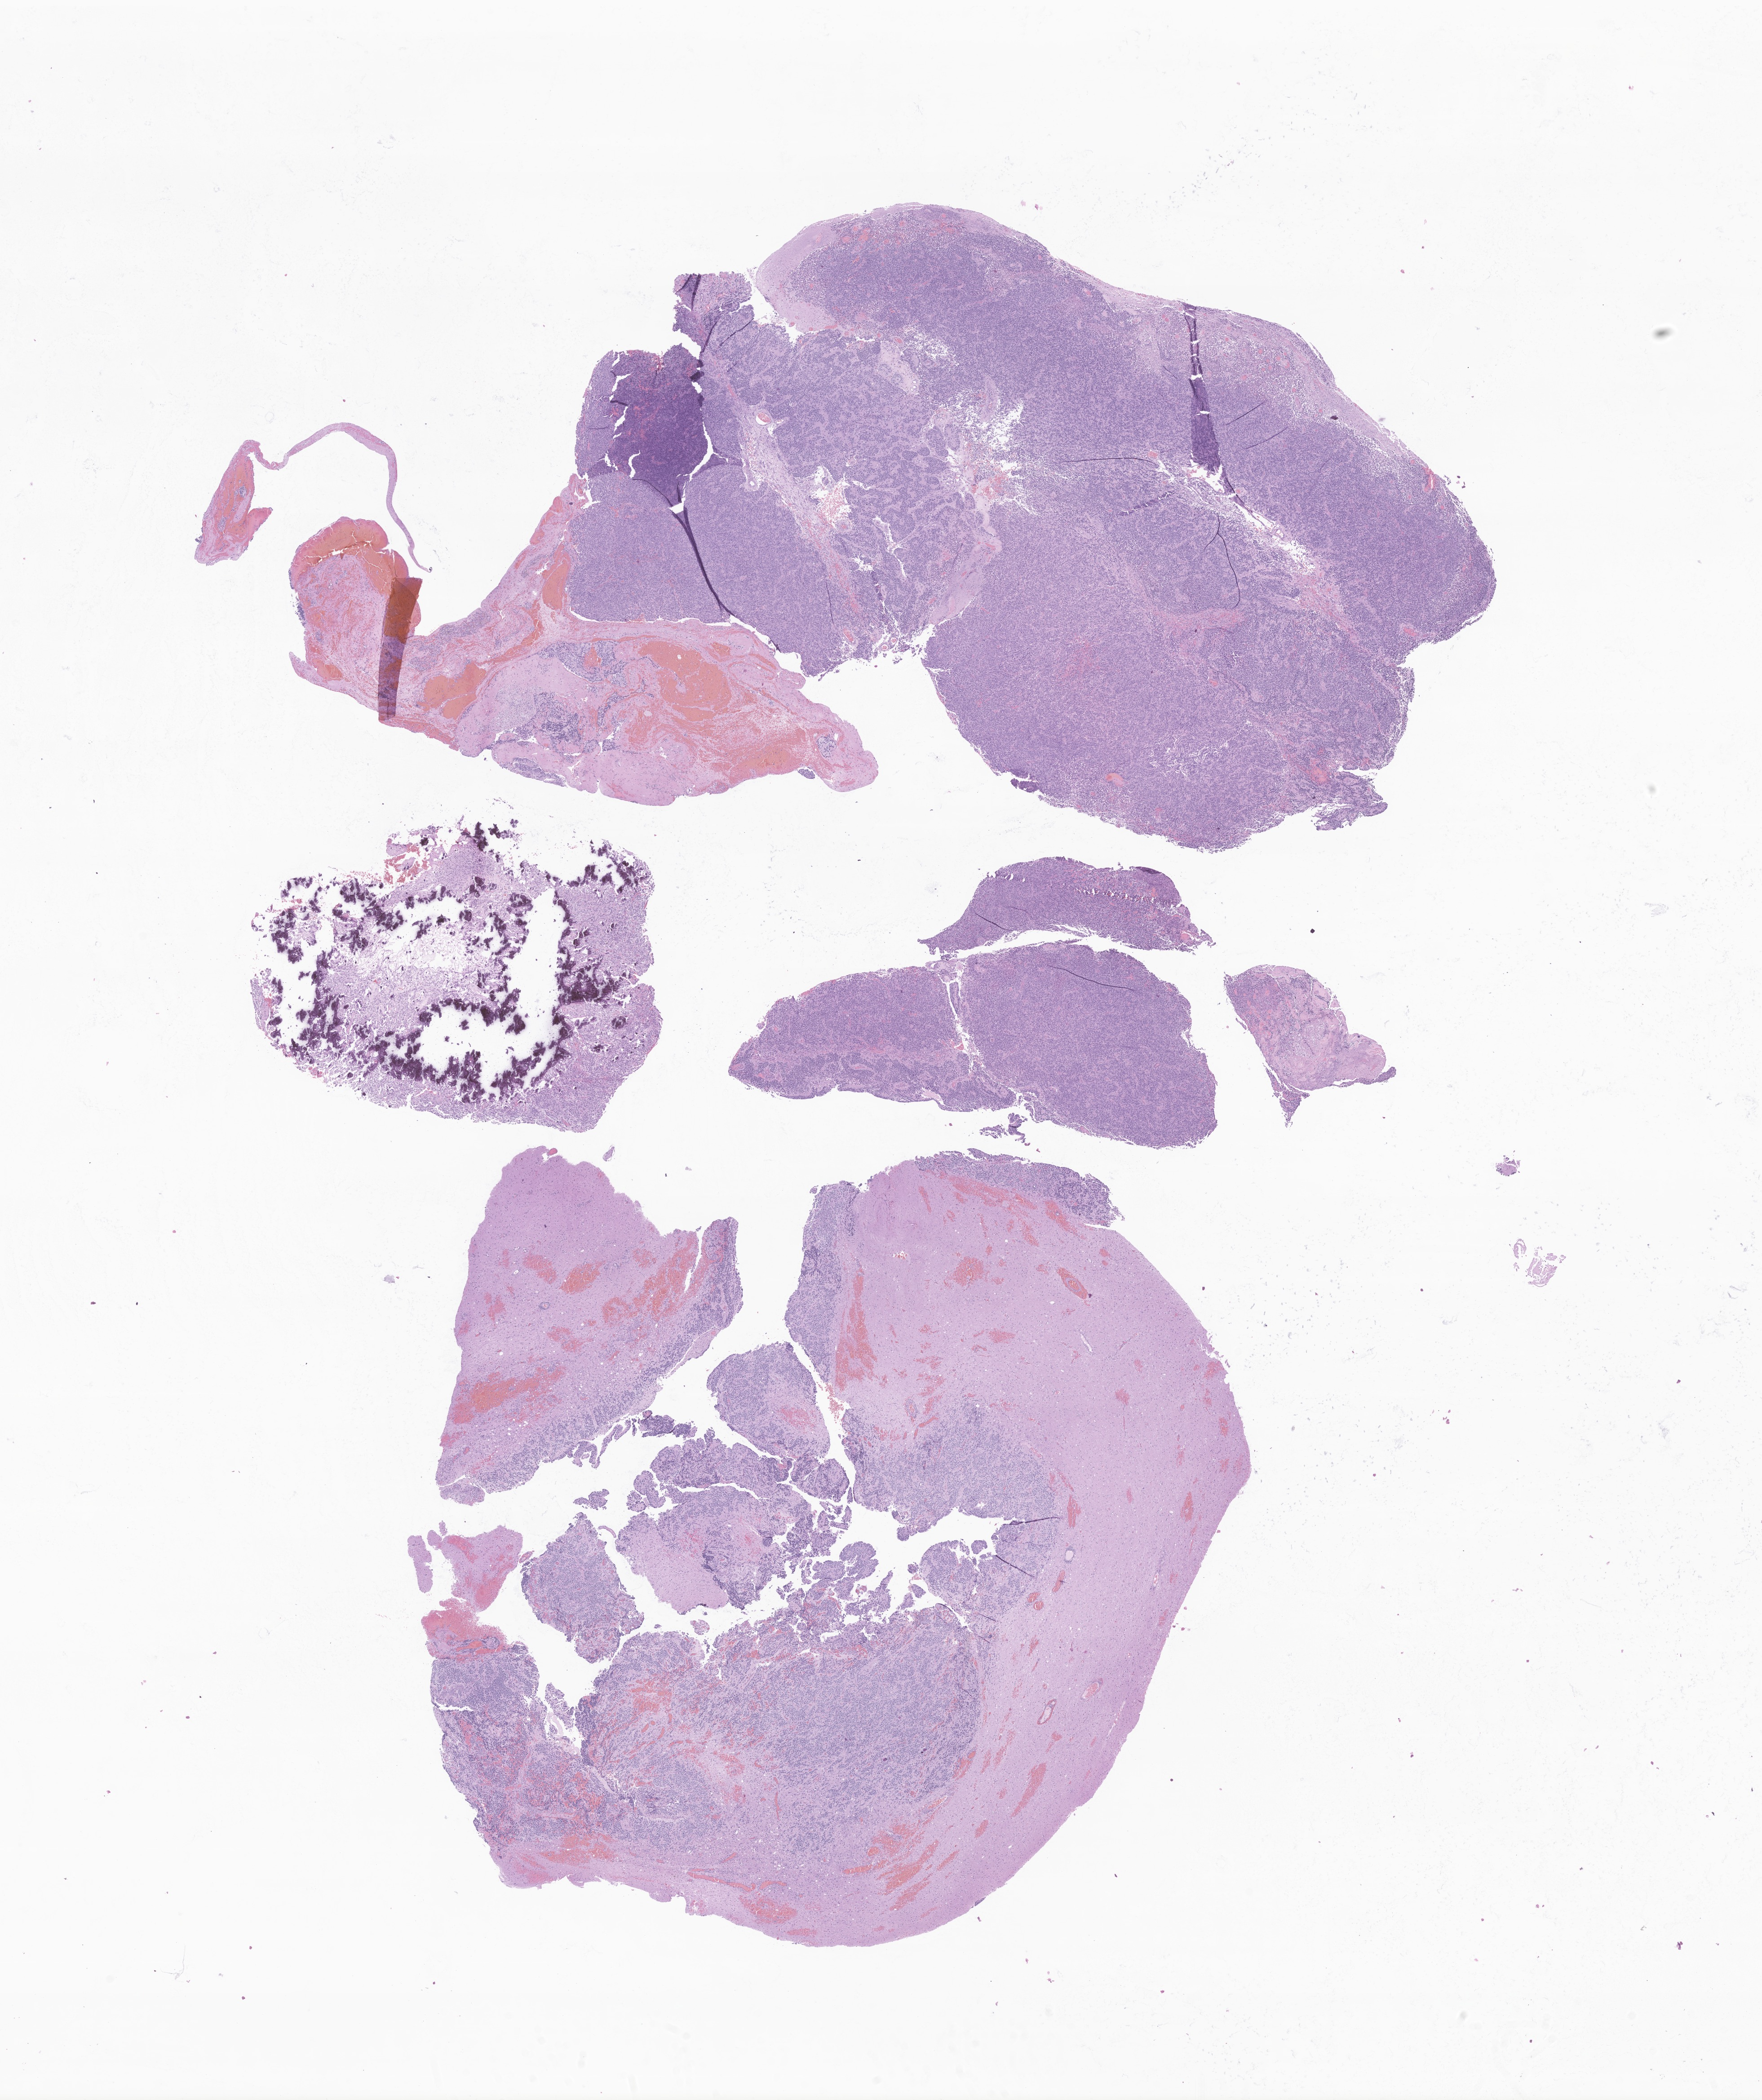
Whole-slide image, haematoxylin and eosin stain of tumor tissue from the occipital lobe, shown as a low-resolution overview of the whole scanned area (about 16.5 x 19.7 mm), formalin-fixed paraffin-embedded section. Female patient, age 124 months (10 years 4 months).
Diagnosis (ICD-O-3 morphology term): Neuroepithelioma, NOS.